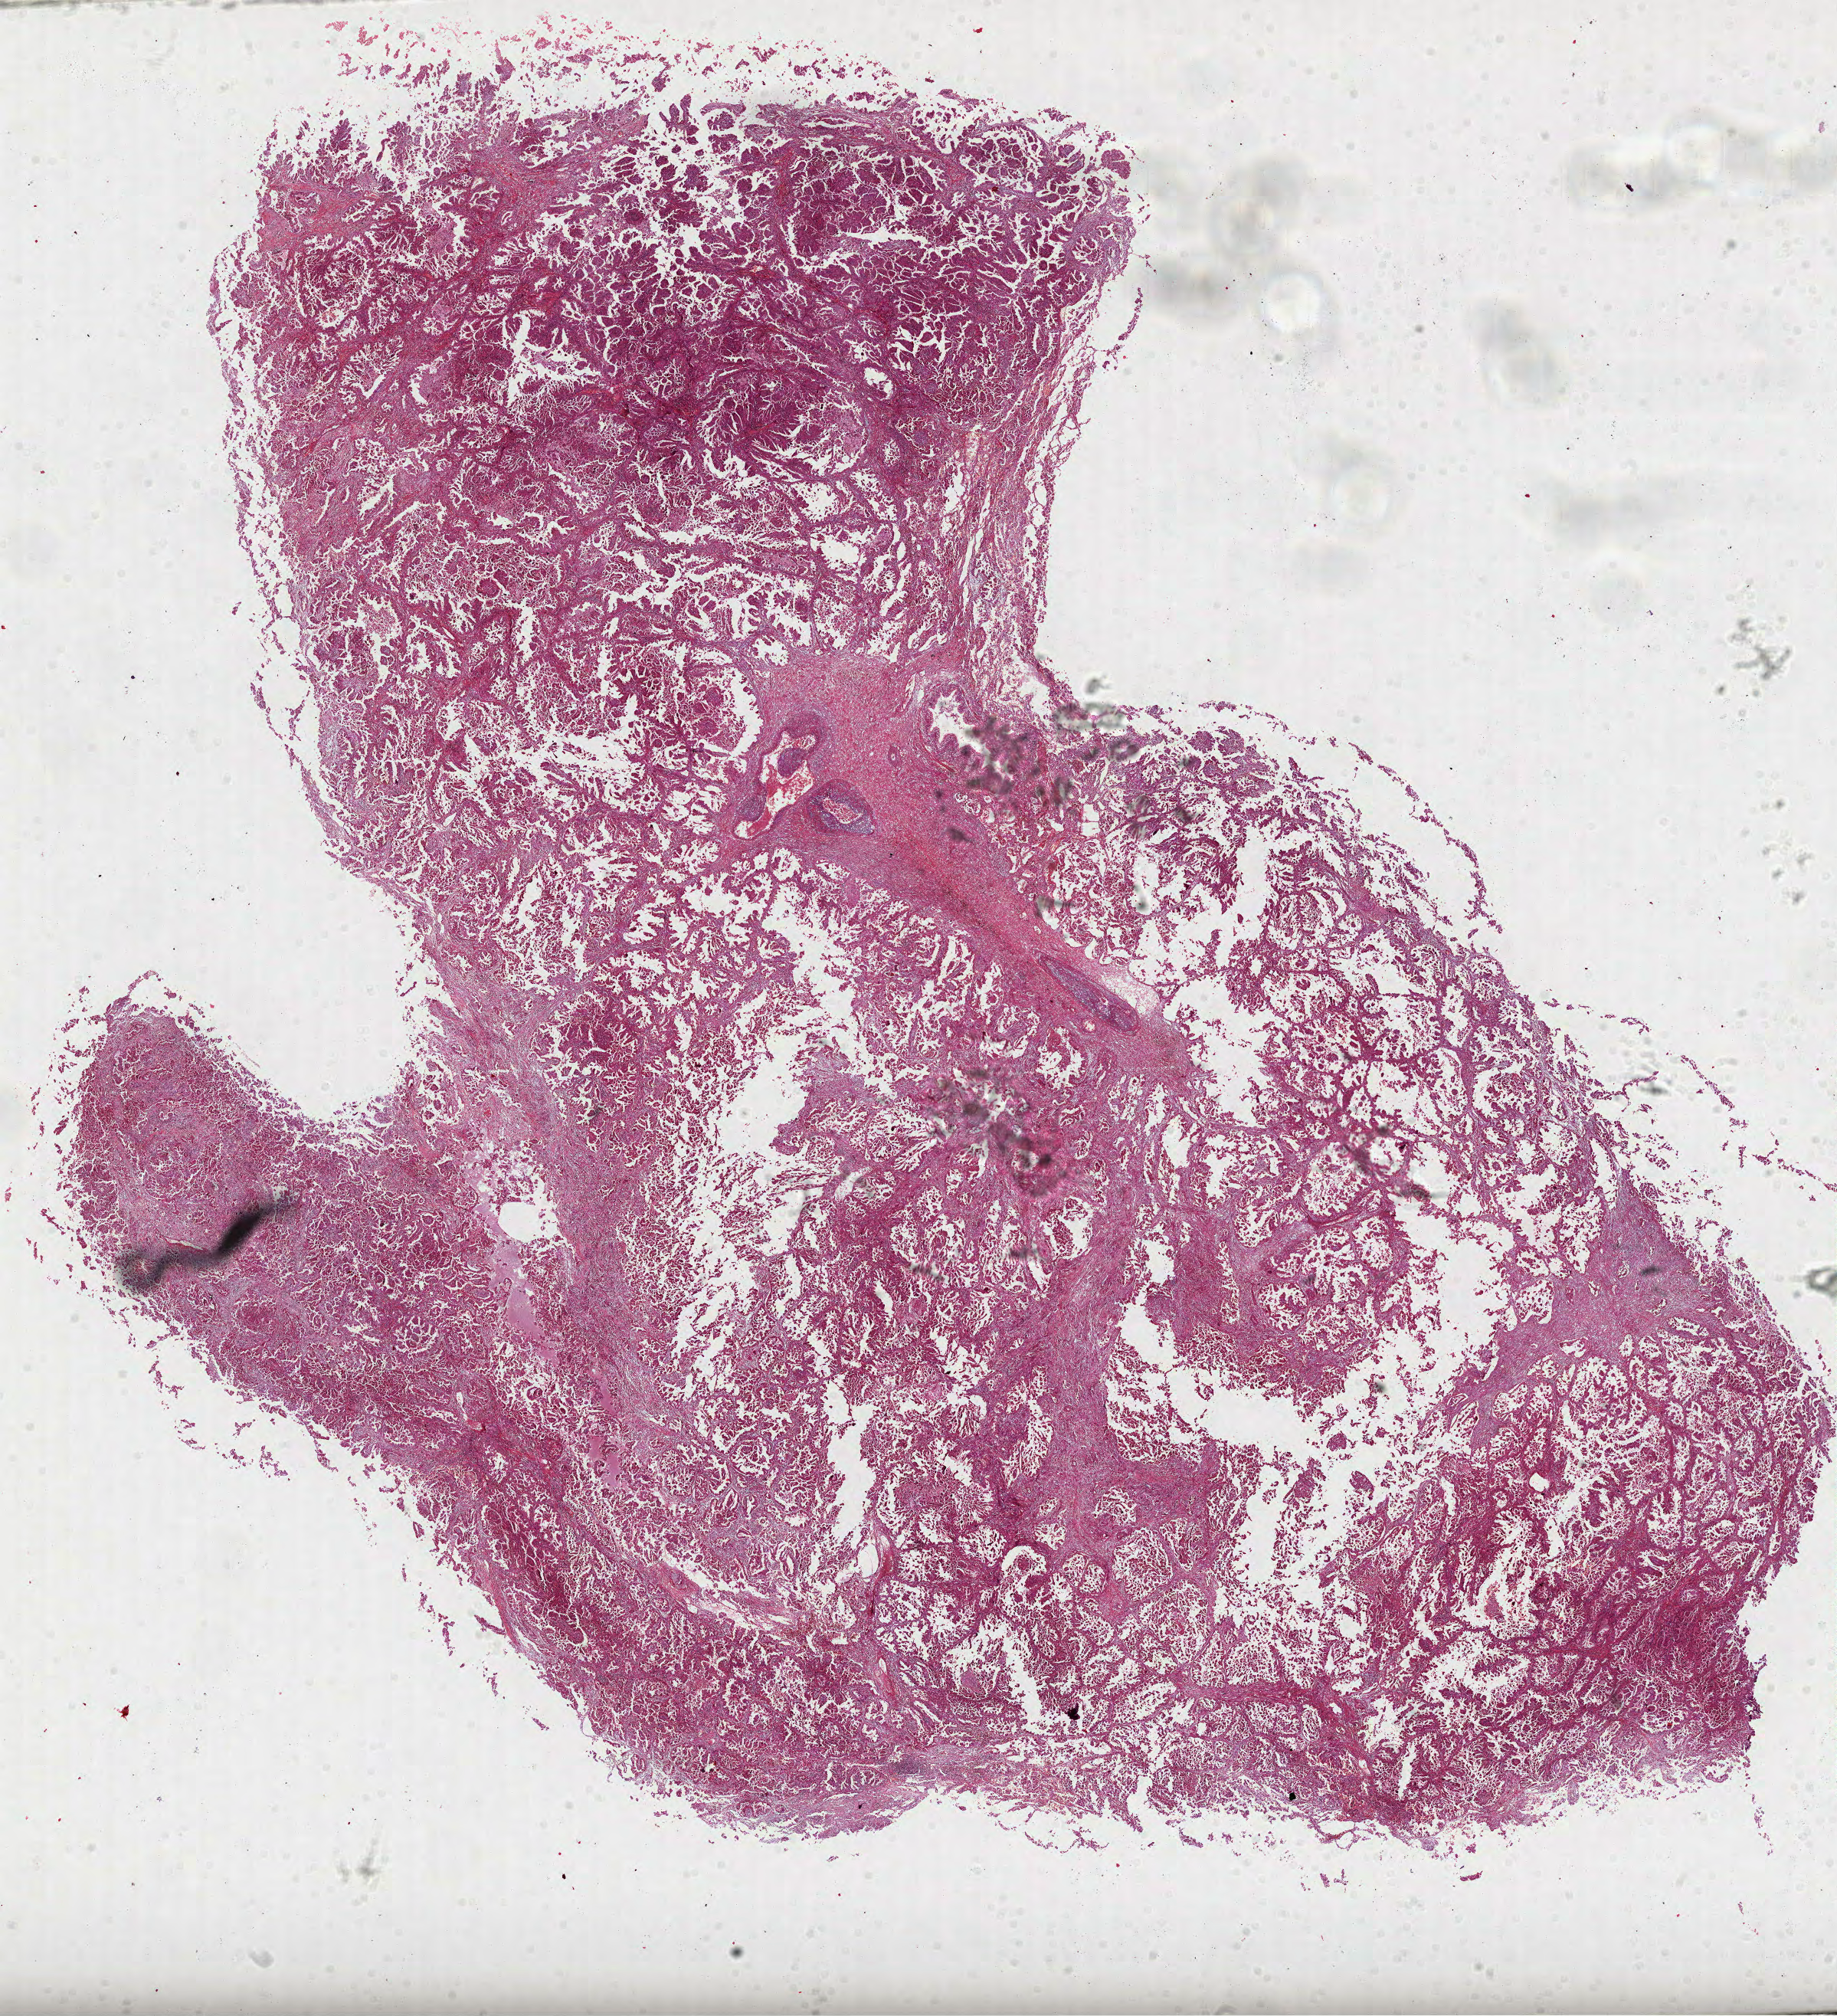
Digitized H&E tissue section (whole slide) — a low-resolution overview of the entire scanned area, about 19.3 x 21.2 mm (acquisition: 40x scan). FFPE section. Primary tumour sample from the lung. Patient: female, age at initial diagnosis 48 years.
• AJCC pathologic stage: IB
• diagnosis: Papillary adenocarcinoma, NOS (upper lobe, lung)